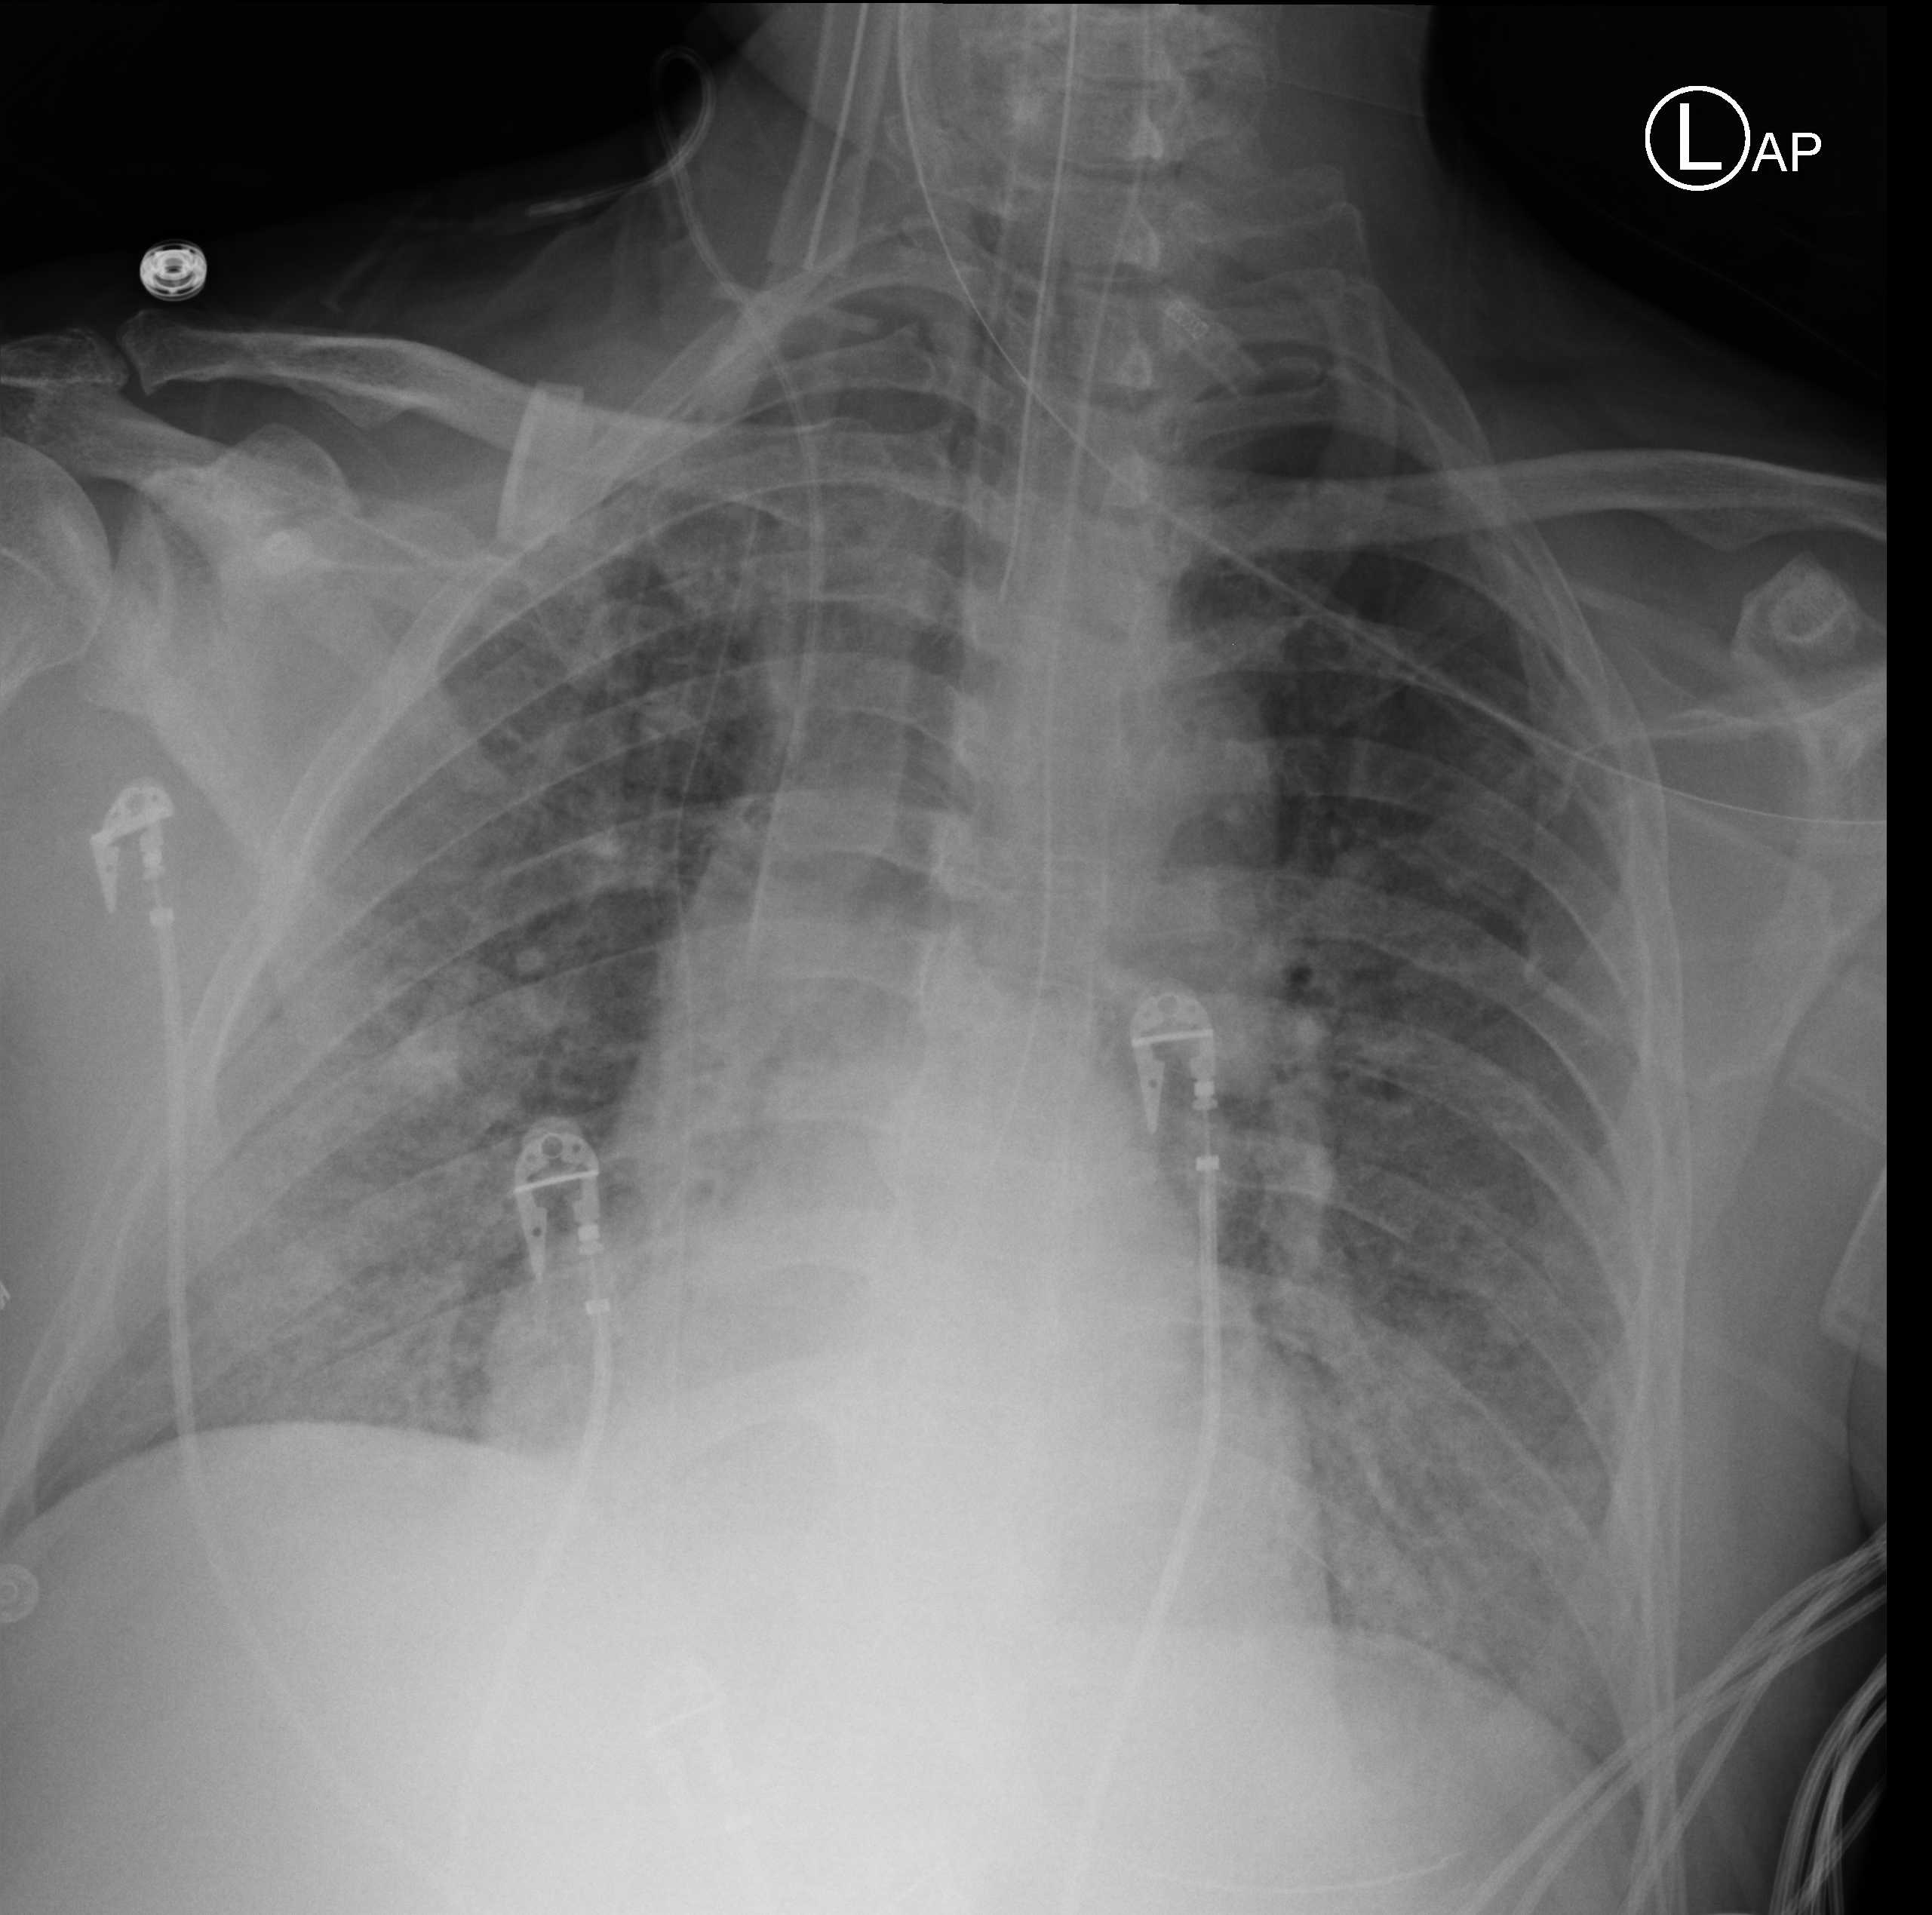
Portable chest radiograph, anteroposterior (AP) projection. Patient hospitalised with COVID-19; male, aged 60–74 years.
Admission-level facts for this patient (not findings on this image; timing relative to this image not recorded): admitted to intensive care during this hospital stay: yes.